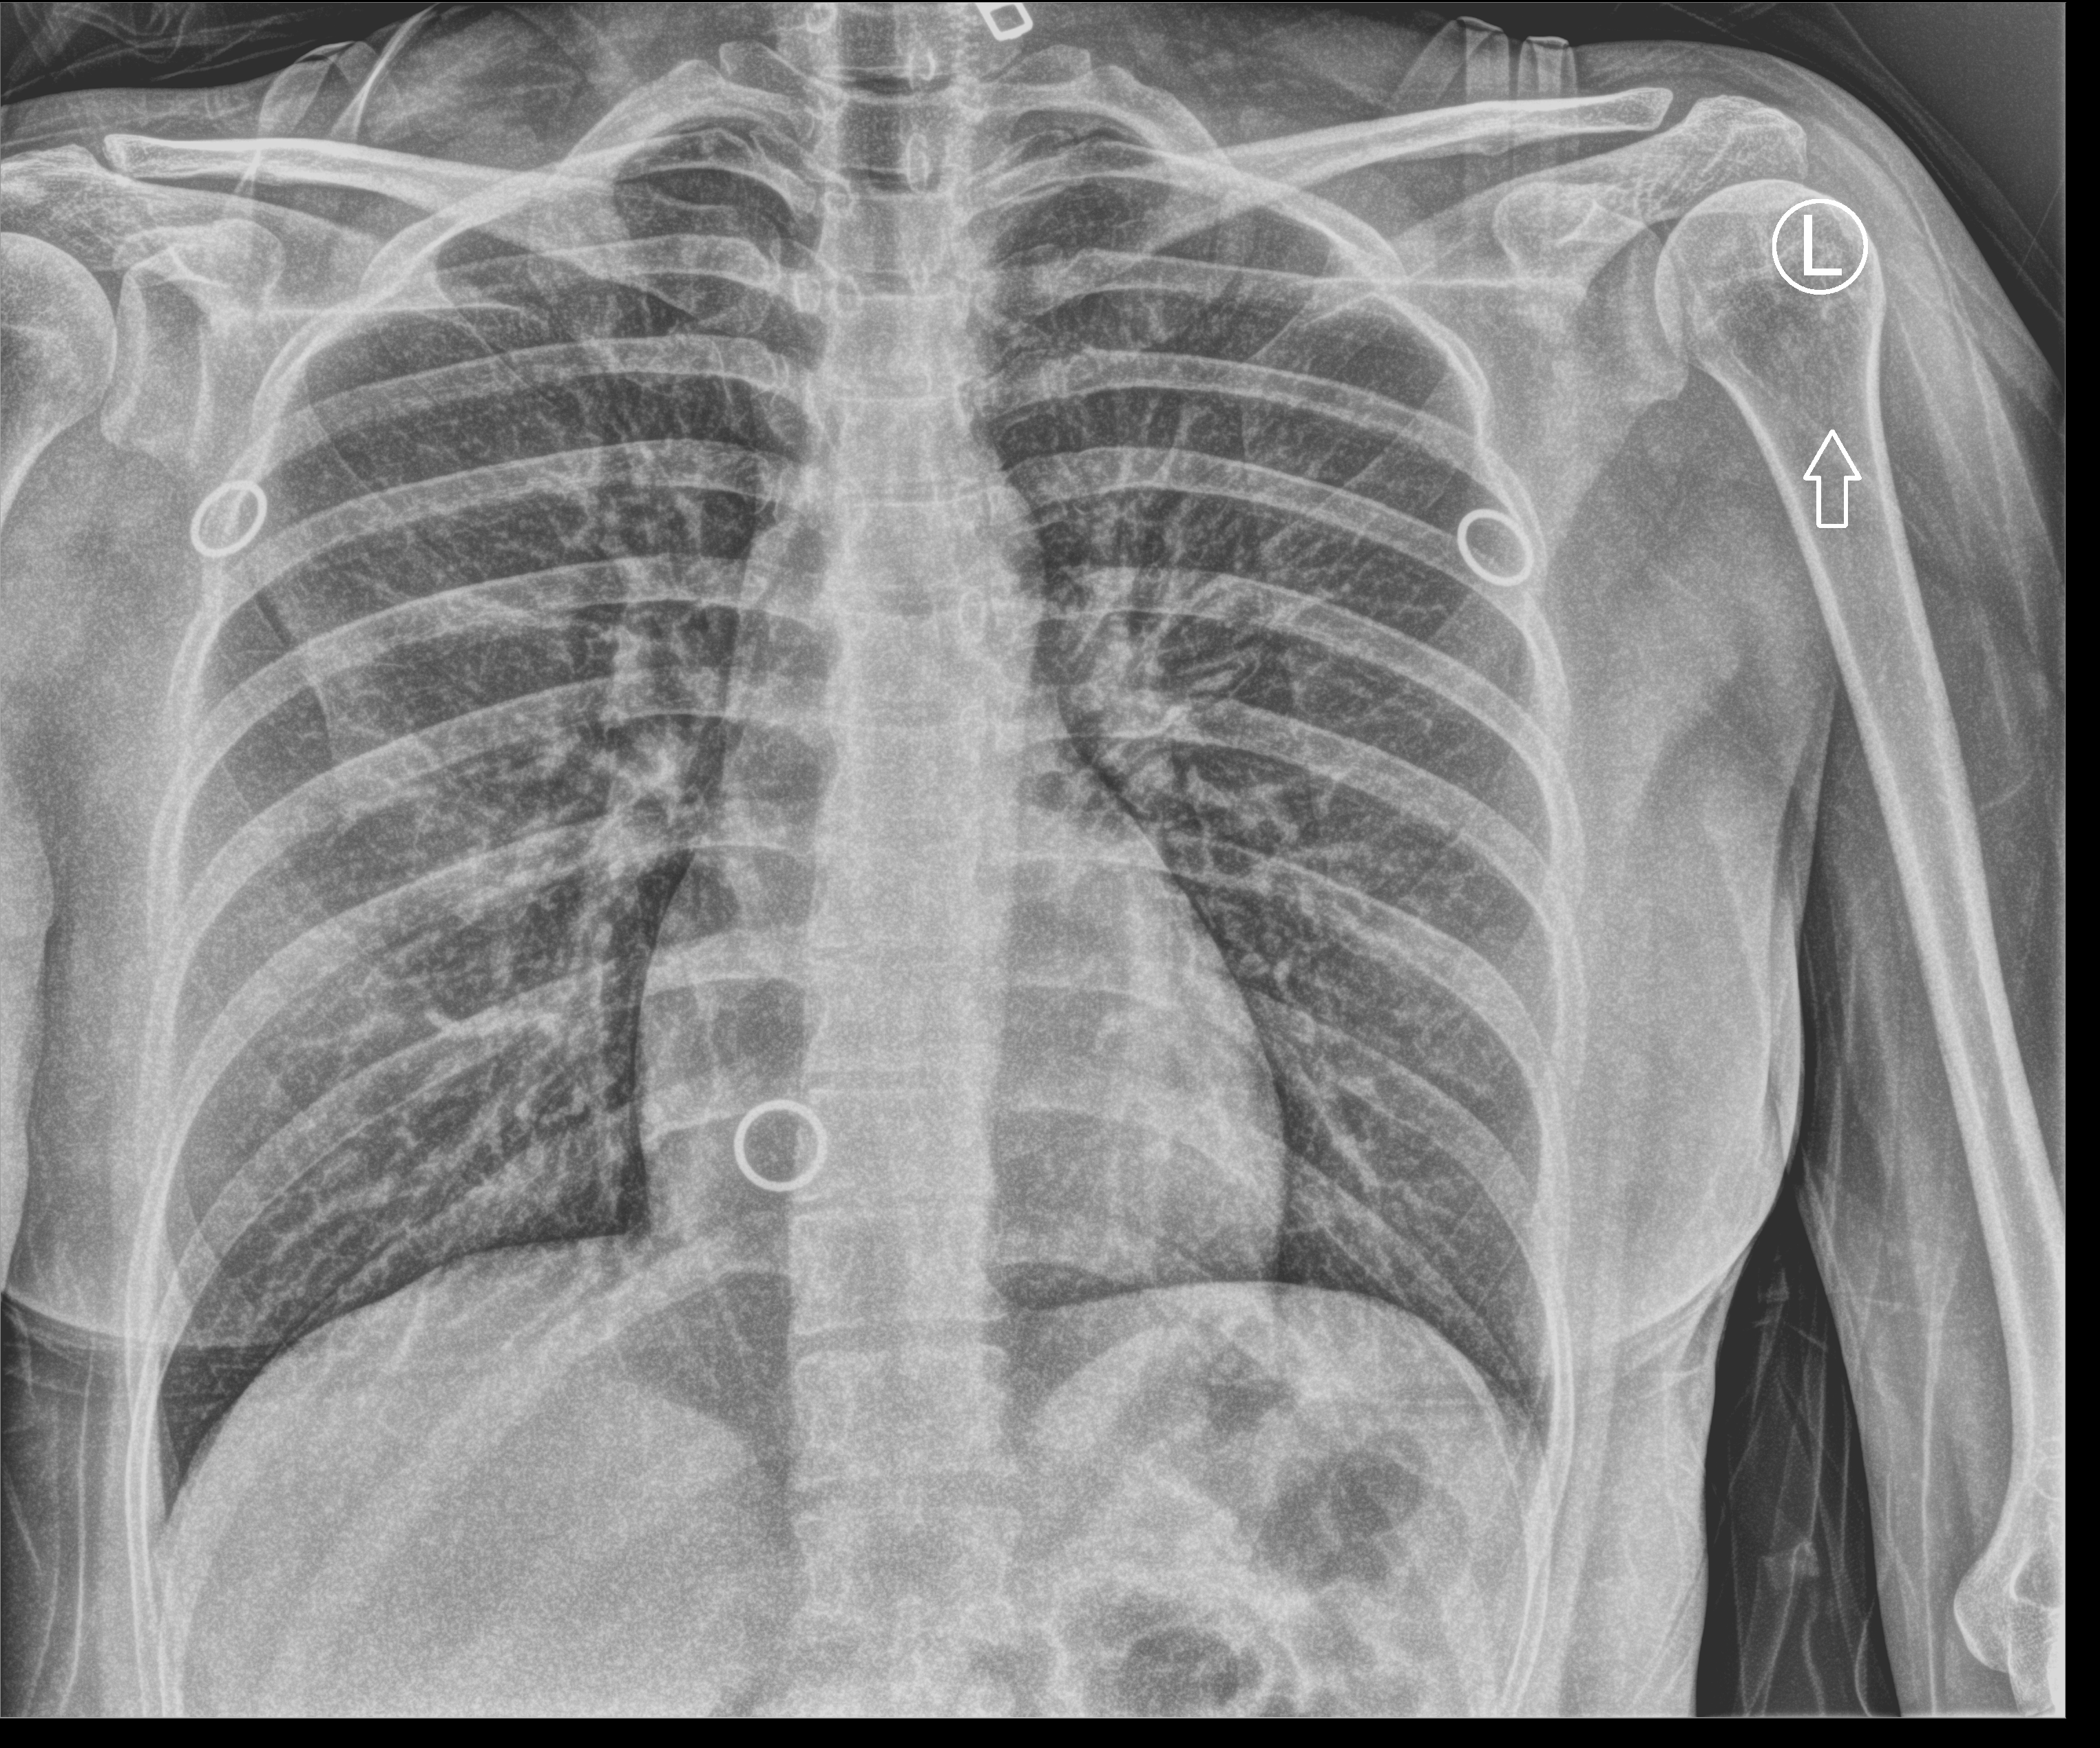
Portable chest radiograph, anteroposterior (AP) projection. Patient hospitalised with COVID-19; female, aged 18–59 years.
From the hospital-stay record, not from the radiograph (when in the stay this image was taken is not recorded):
- admitted to intensive care during this hospital stay: no
- mechanically ventilated during this hospital stay: no